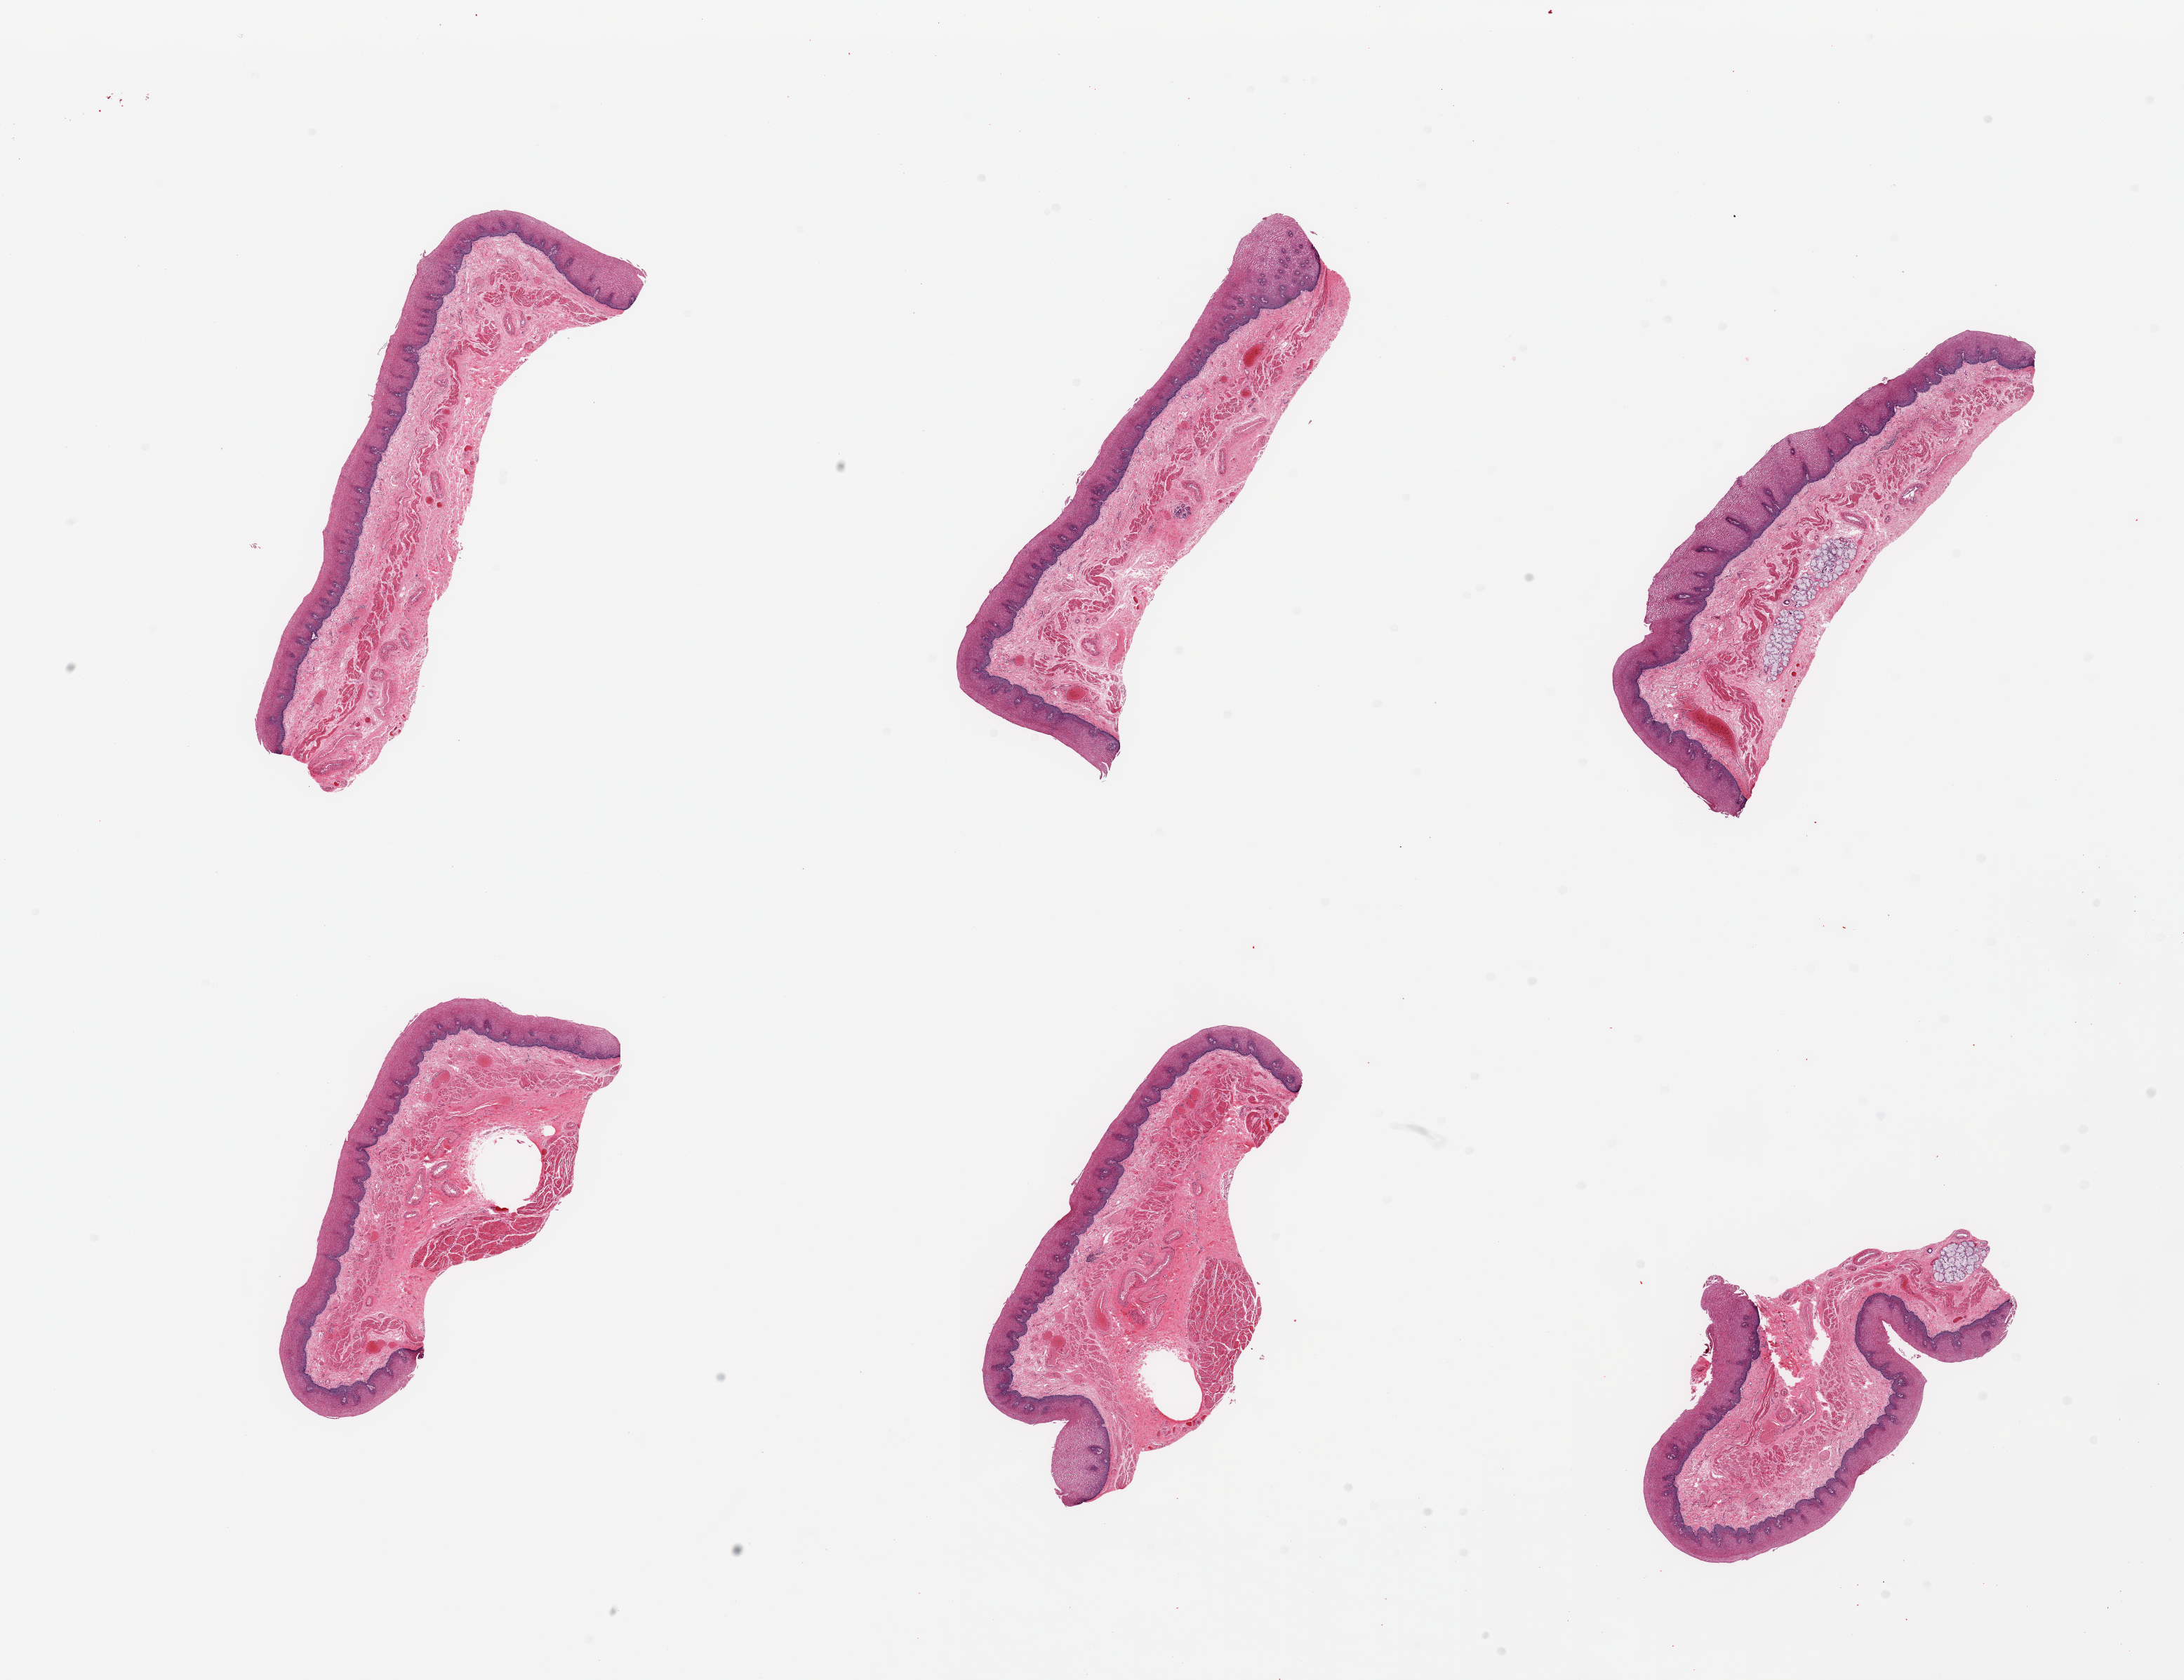
Haematoxylin and eosin whole-slide image — a low-resolution overview of the entire scanned area, about 24.6 x 18.9 mm (acquisition: 20x scan); PAXgene-fixed paraffin-embedded (PFPE) section; section of esophageal mucous membrane (target tissue); tissue donor sample. Male donor.
- reviewer comment on this tissue sample: 6 pieces; well preserved epithelium; submucosal glands in 2 pieces up to 10% area